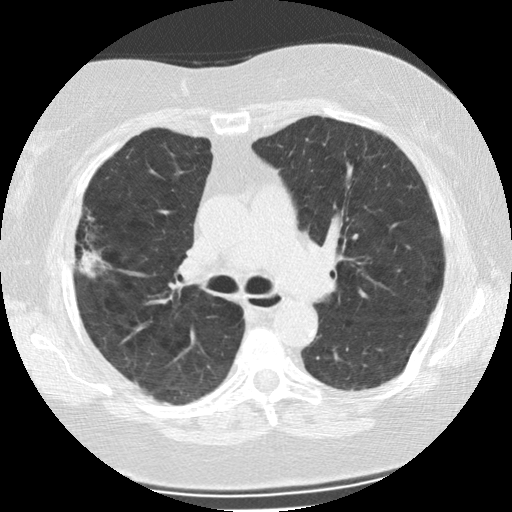
Low-dose screening chest CT, one axial slice. Slice 145 of 225 in the series (ordered by position). 120 kVp. Lung window (W 1500 / L -600 HU). 2.5 mm slice thickness. 512 × 512 image matrix.
Outlined on this slice (manually delineated by an expert):
- lesion 1 (tumor, upper lobe of right lung): bounding box (x1, y1, x2, y2) in pixels: (79, 250, 103, 277)